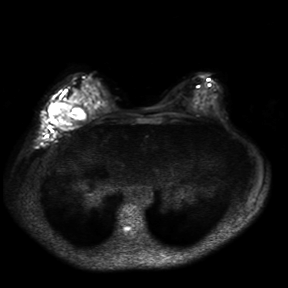
Breast MRI, one axial slice; slice 16 of 30 in the series (ordered by position); diffusion-weighted series; image 2 of 4 stored at this slice position (different b-values; order by instance number); 3 T; 4 mm slice thickness; 288 × 288 image matrix, field of view 360 × 360 mm. Female patient.
Annotated regions visible in this slice (expert manual segmentation):
- tumour on diffusion-weighted imaging: box from (x=49, y=103) to (x=85, y=124) px